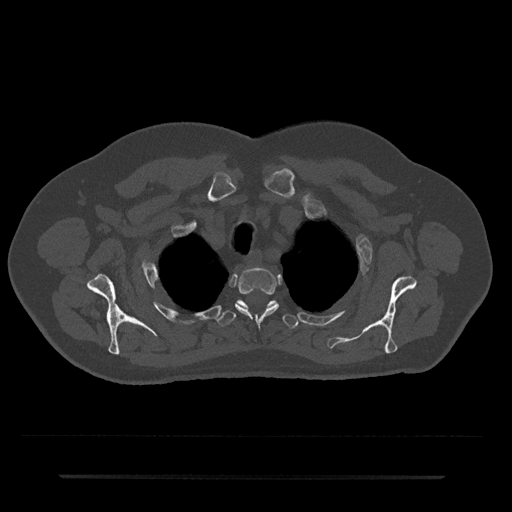
CT including the spine, one axial slice; position 593 of 797 along the scan axis; reconstruction kernel Br40s/3; 120 kVp; bone window (W 1800 / L 400 HU); 512 × 512 image matrix, field of view 437 × 437 mm. Patient: male, 69 years. Case-level facts recorded for this patient, not image findings: primary cancer: prostate.
Outlined on this slice (semi-automatically segmented with operator editing):
- T2 vertebra: bounding box [x1, y1, x2, y2] px = [235, 268, 279, 320]
- T3 vertebra: [217, 300, 298, 329]